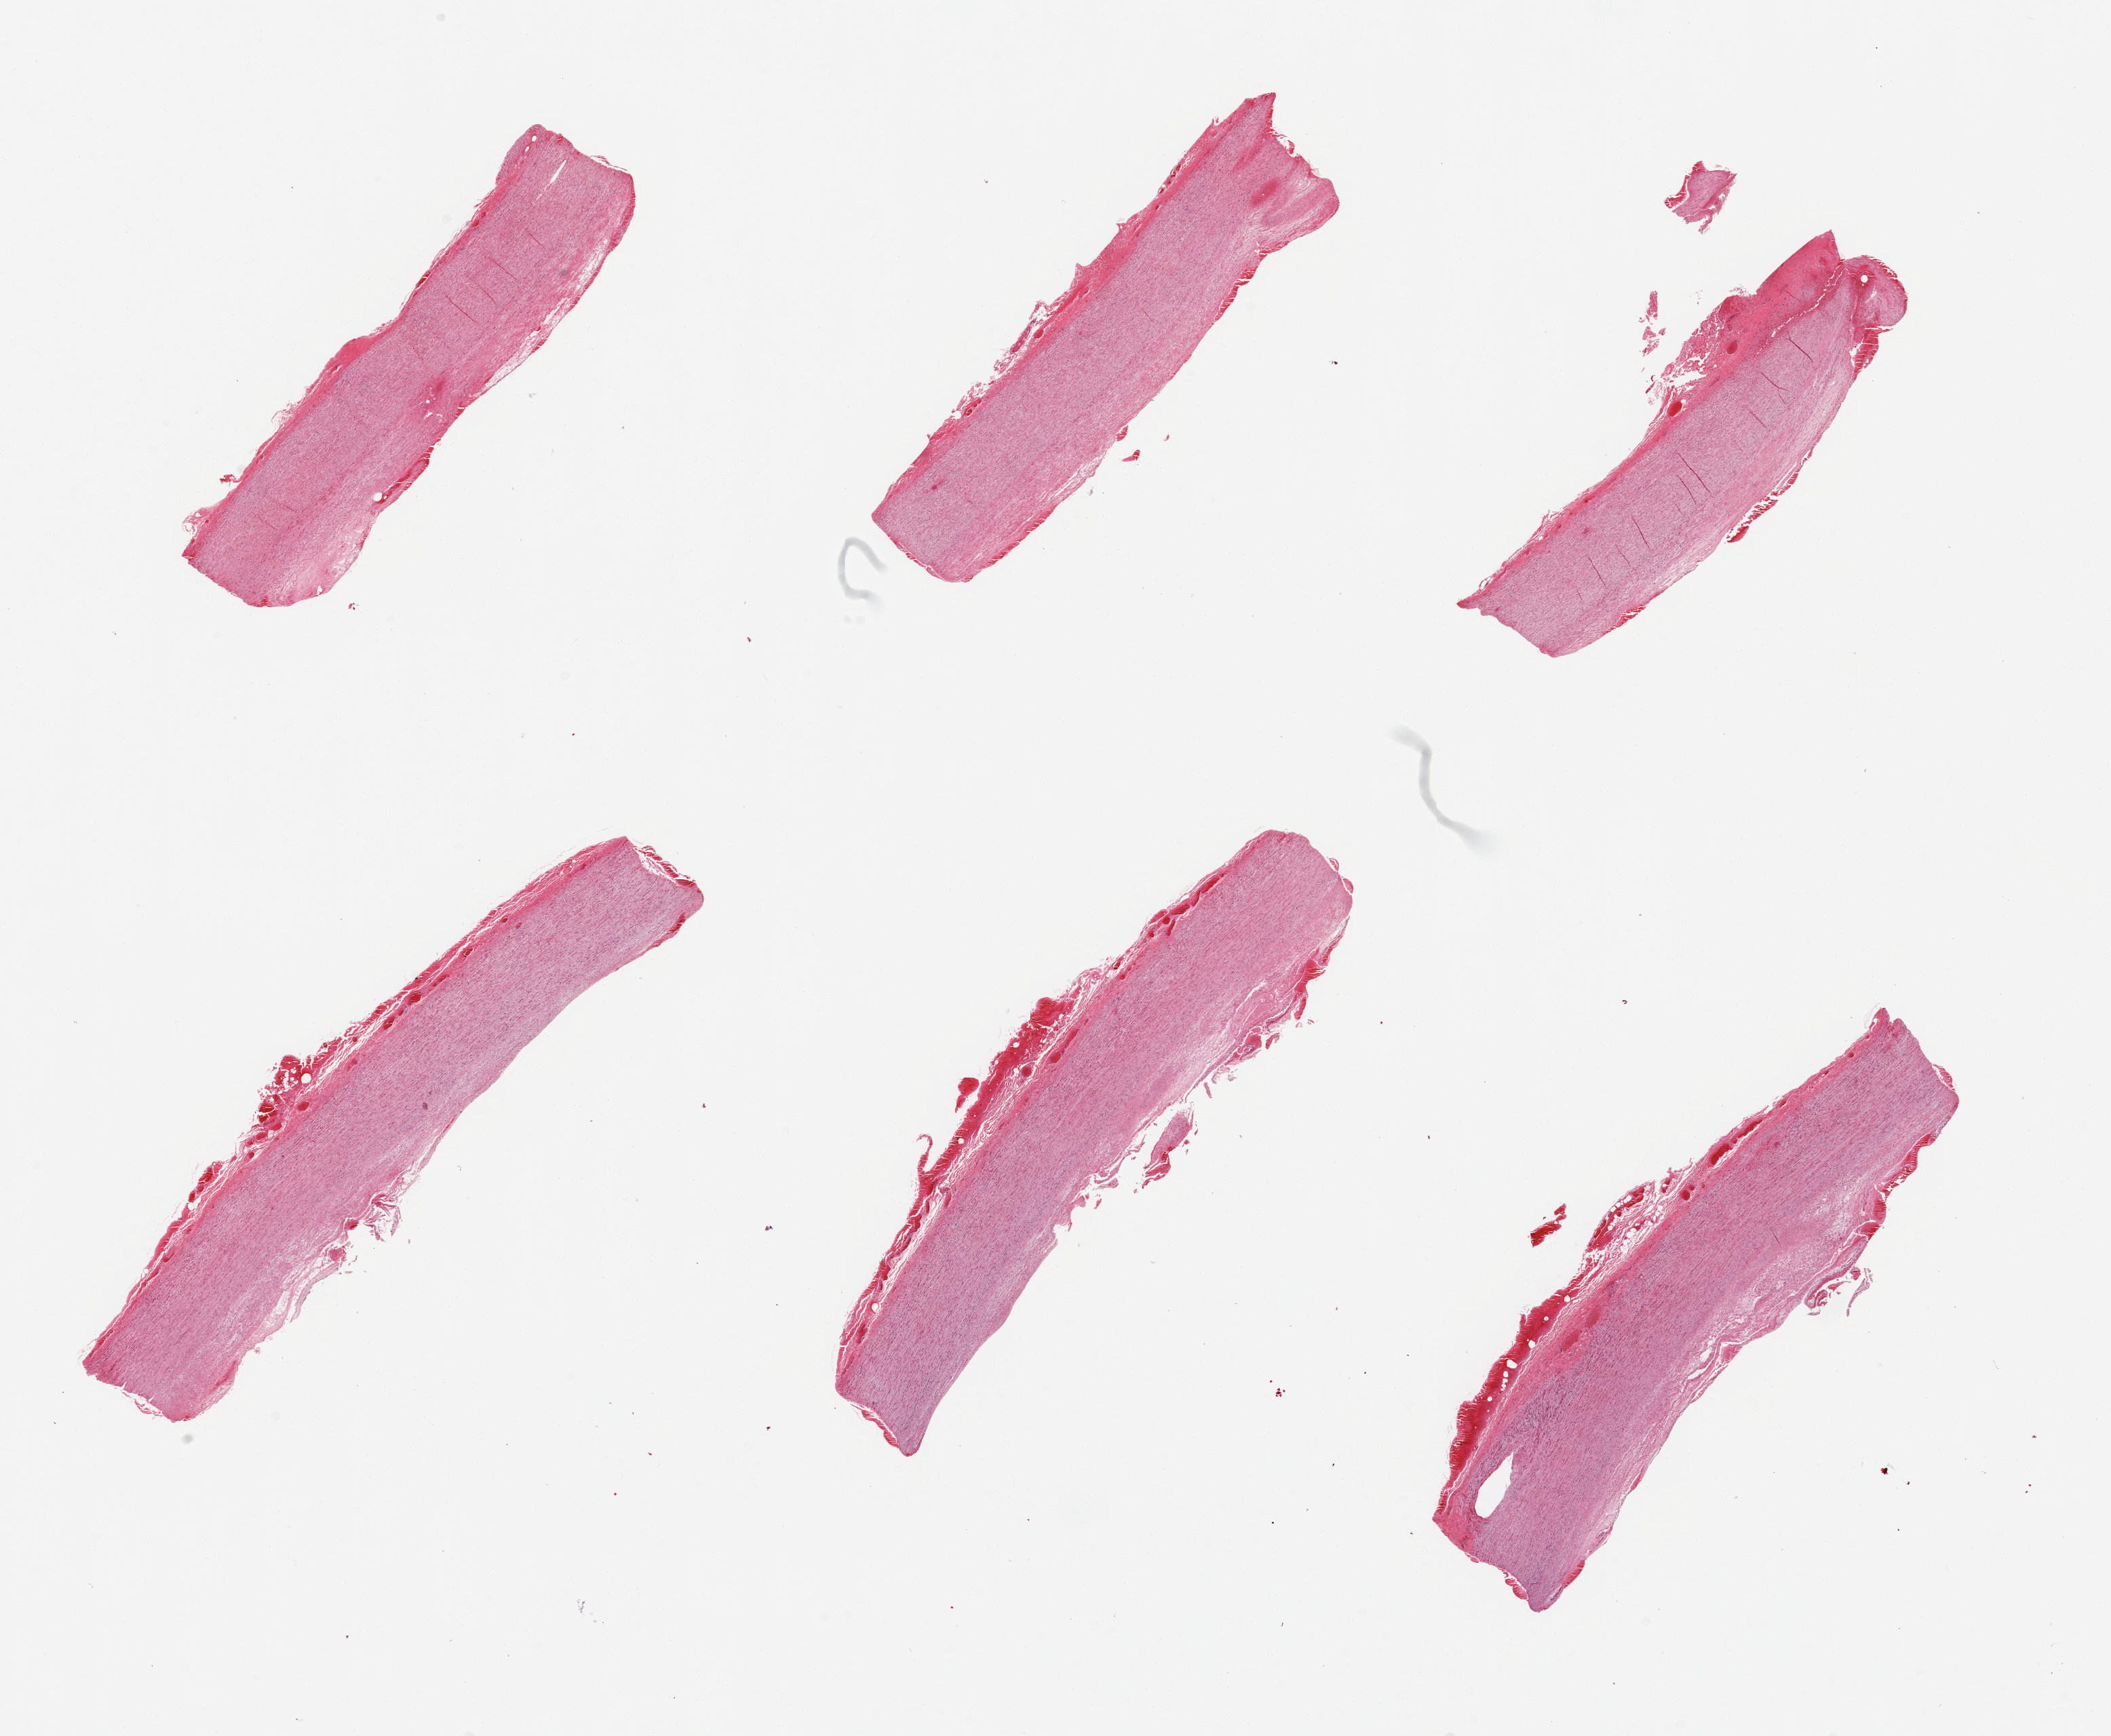
Digitized H&E-stained section — shown as a low-resolution overview of the whole scanned area (about 24.6 x 20.2 mm); PAXgene-fixed paraffin-embedded (PFPE) section; sampled site (target tissue): aorta; tissue donor sample. Donor: male.
Pathologist's review note for this sample: 6 pieces, hemorrhage in adventitia, atherosclerosis.